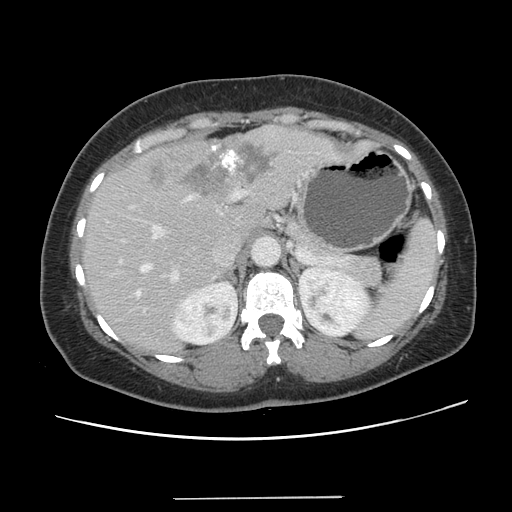
Contrast-enhanced abdominal CT, one axial slice; slice 88 of 141 in the series (ordered by position); intravenous contrast given; soft-tissue window (W 400 / L 40 HU); 2.5 mm slice thickness; 512 × 512 image matrix, field of view 366 × 366 mm. Female patient, age 53 years. From the clinical record (not read from this slice): diagnosis: colorectal cancer liver metastases, imaged before liver resection; multiple liver metastases: no; largest metastasis: 14.5 cm; disease in both lobes: yes.
Annotated regions visible in this slice (outlined manually by an expert reader):
- hepatic veins: box from (x=136, y=197) to (x=191, y=296) px
- liver: (x=83, y=126)–(x=370, y=353)
- planned liver remnant (the part of the liver to remain after resection): (x=84, y=207)–(x=263, y=352)
- portal vein (with intrahepatic branches): (x=152, y=189)–(x=243, y=284)
- liver metastasis: (x=146, y=142)–(x=279, y=195)